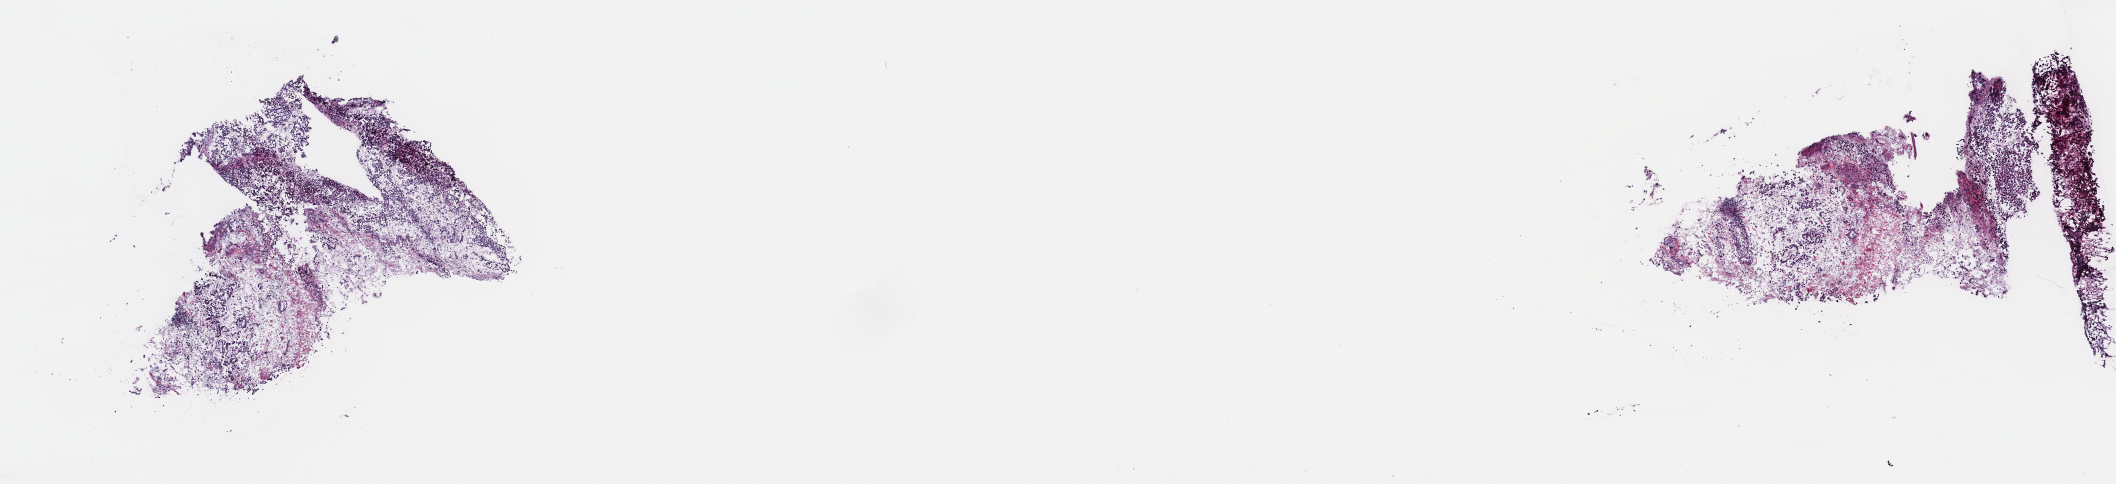
Hematoxylin and eosin (H&E) stained whole-slide image, shown as a low-resolution overview of the whole scanned area (about 17.1 x 3.9 mm). Frozen section from the top of the tissue portion. Mesothelium, primary tumour sample. Male patient; age at initial diagnosis 70 years. Pathologist review of this section (percent, as recorded): tumour cells 60%, tumour nuclei 60%, normal cells 0%, stromal cells 20%, necrosis 20%. Inflammatory infiltration, as recorded: lymphocyte infiltration 40%, monocyte infiltration 20%, neutrophil infiltration 20%.
• diagnosis: Epithelioid mesothelioma, malignant (pleura, NOS)
• laterality: left
• AJCC pathologic stage: II (7th edition)